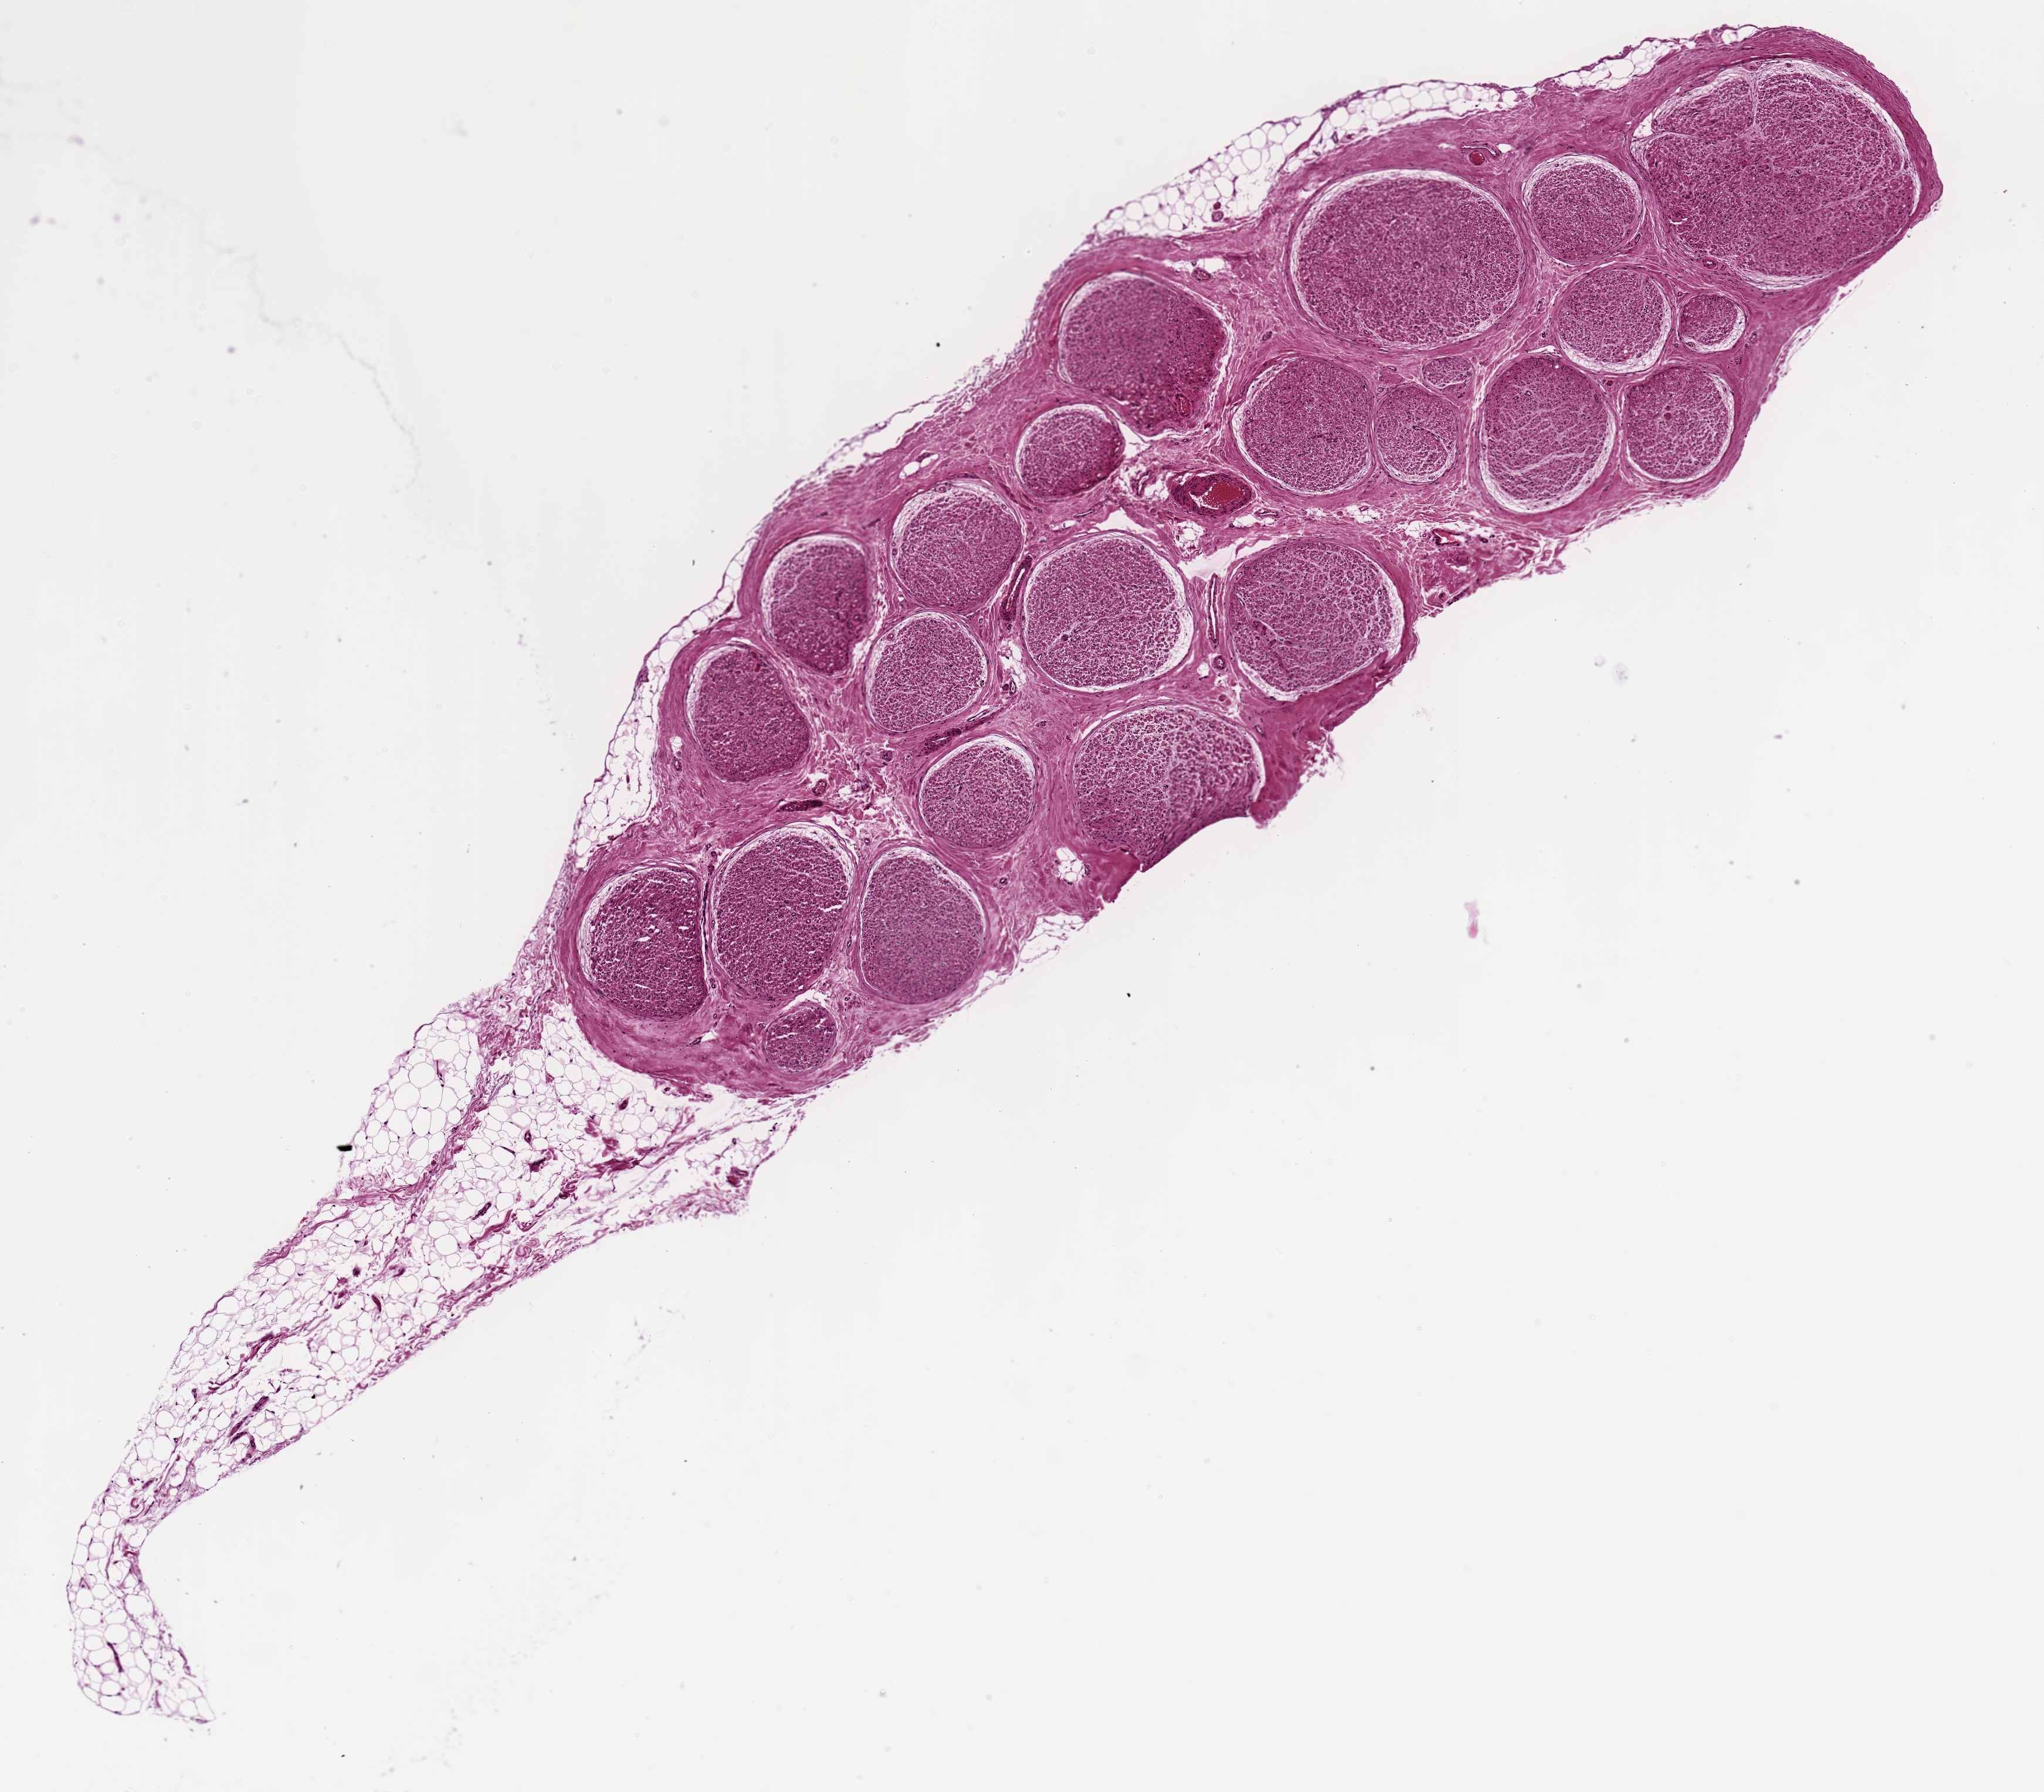
Whole-slide image, hematoxylin and eosin (H&E) stain — whole scanned area (about 6.9 x 6.0 mm, acquisition: 20x scan) shown as a low-resolution overview, PAXgene-fixed, paraffin-embedded tissue, section of tibial nerve (target tissue), donor tissue sample. Donor sex: female.
Review note (as recorded): 5x1.7 mm; 2.5 mm fatty tail.